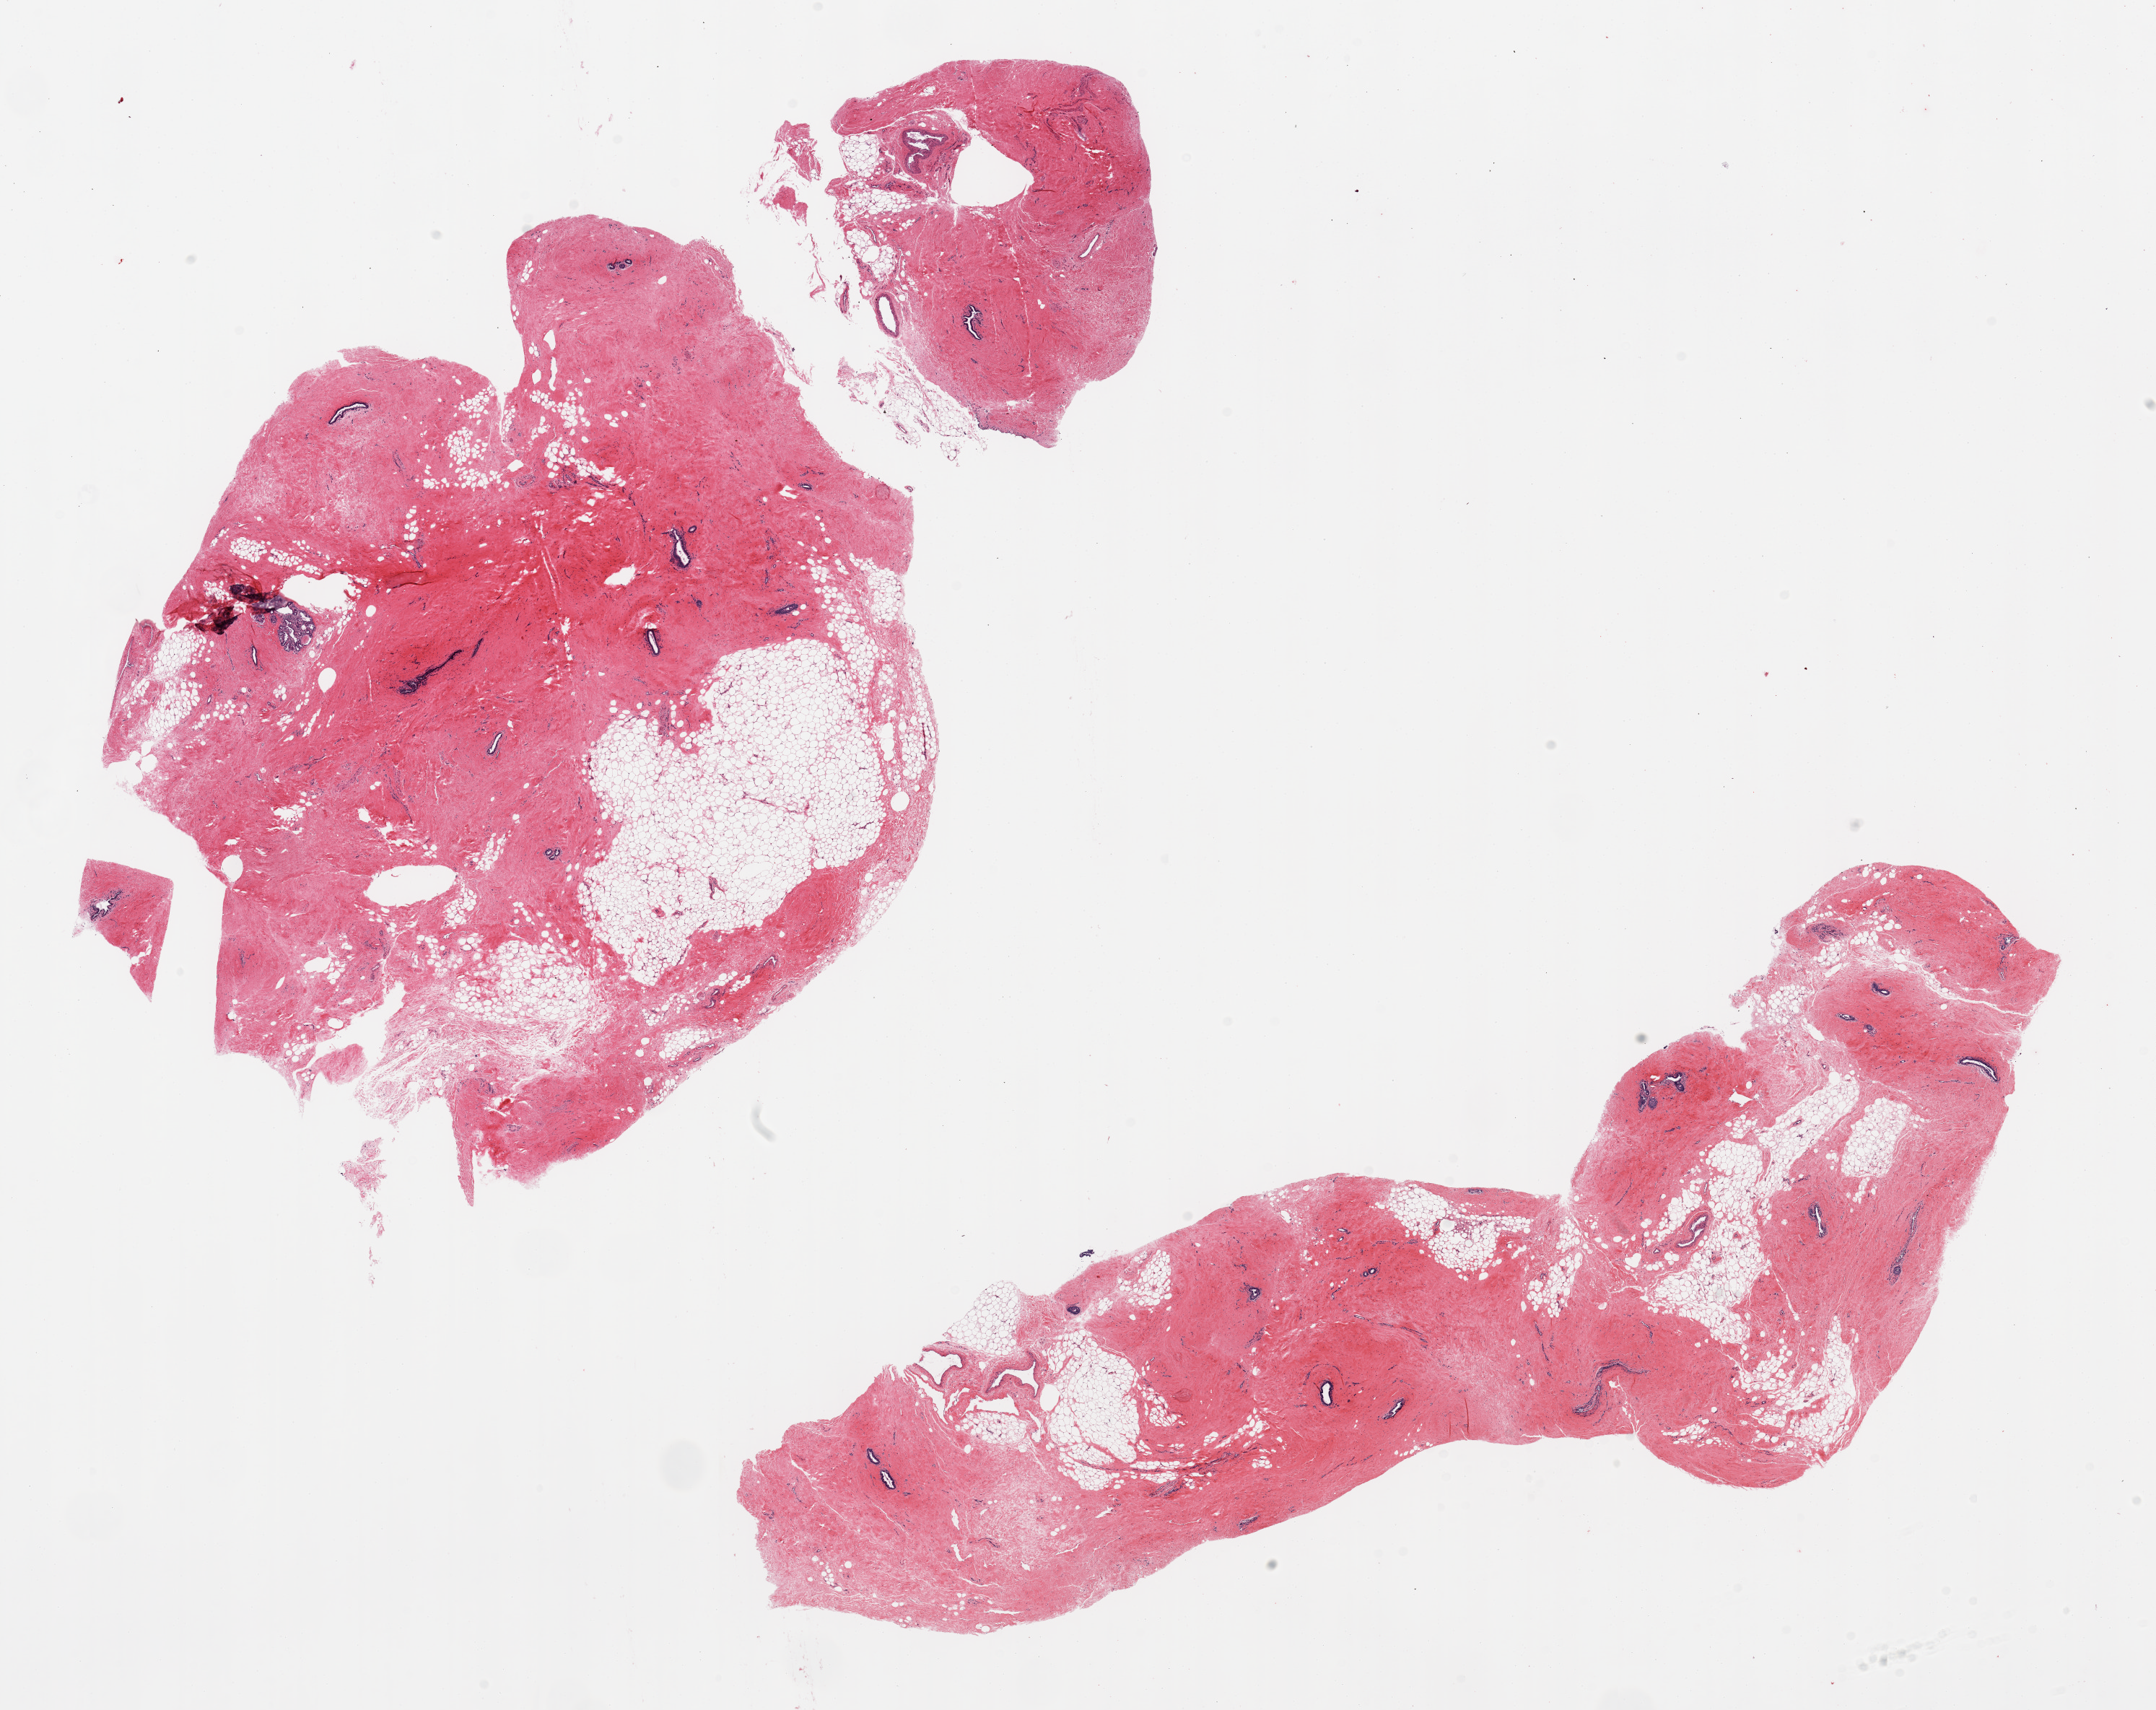
Digitized haematoxylin and eosin-stained section, low-resolution overview of the scanned area, about 23.6 x 18.7 mm (slide scanned at 20x). PAXgene-fixed, paraffin-embedded tissue. Sampled site (target tissue): breast. Donor tissue sample. Donor: male.
Reviewer comment on this tissue sample: 2 pieces; gynecomastoid change.